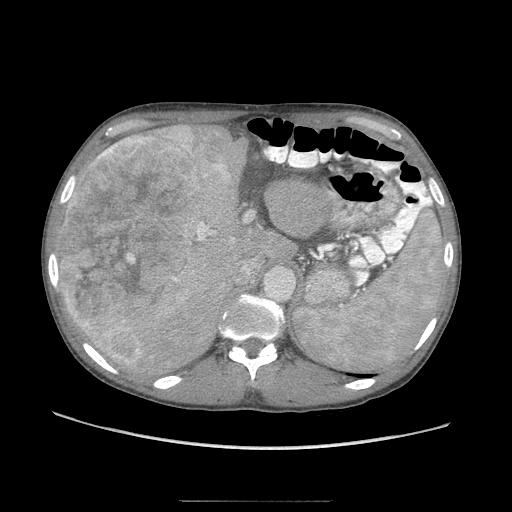
Contrast-enhanced abdominal CT (liver protocol), one axial slice. 120 kVp. Soft-tissue window (W 400 / L 40 HU). 2.5 mm slice thickness. 512 × 512 image matrix, field of view 380 × 380 mm. Case-level facts recorded for this patient, not image findings: diagnosis: hepatocellular carcinoma (patient treated with transarterial chemoembolisation; whether this scan precedes or follows treatment is not stated here); TNM stage (as recorded): Stage-IIIA; Child-Pugh class: A.
Annotated regions visible in this slice (semi-automatically segmented with operator editing):
- liver parenchyma outside the tumour (the mass and vessels are separate outlines, so this box may not span the whole liver): bounding box <58,124,316,380> (left, top, right, bottom; pixels)
- mass: <58,132,233,364>
- liver vessels: <110,223,213,372>